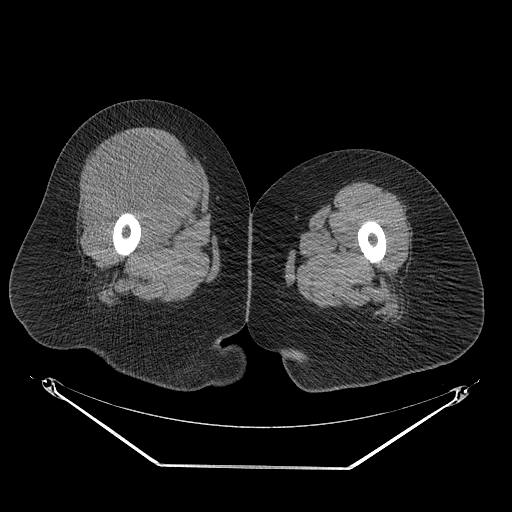
CT of an extremity soft-tissue mass (from a PET/CT study), one axial slice. Position 36 of 267 along the scan axis. Reconstruction kernel STANDARD. 140 kVp. Soft-tissue window (W 400 / L 40 HU). 3.75 mm slice thickness. 512 × 512 image matrix. Female patient. Case-level facts recorded for this patient, not image findings: histological type: malignant solitary fibrous tumor; grade: intermediate; site of the primary tumour: right thigh.
Structures marked on this image (expert contour drawn on MRI and transferred to this co-registered scan by the dataset authors):
- gross tumour volume including surrounding oedema: box from (x=85, y=133) to (x=207, y=227) px
- gross tumour volume (mass): (x=91, y=133)–(x=204, y=223)